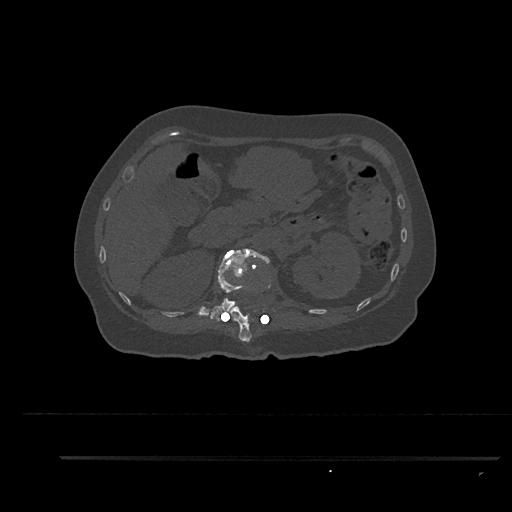
CT including the spine, one axial slice. 120 kVp. Bone window (W 1800 / L 400 HU). 512 × 512 image matrix, field of view 408 × 408 mm. Patient: female, 44 years. Case-level facts recorded for this patient, not image findings: primary cancer: renal.
Annotated regions visible in this slice (semi-automatically segmented with operator editing):
- L1 vertebra: bounding box <209,248,270,320> (left, top, right, bottom; pixels)
- T12 vertebra: <215,283,271,343>